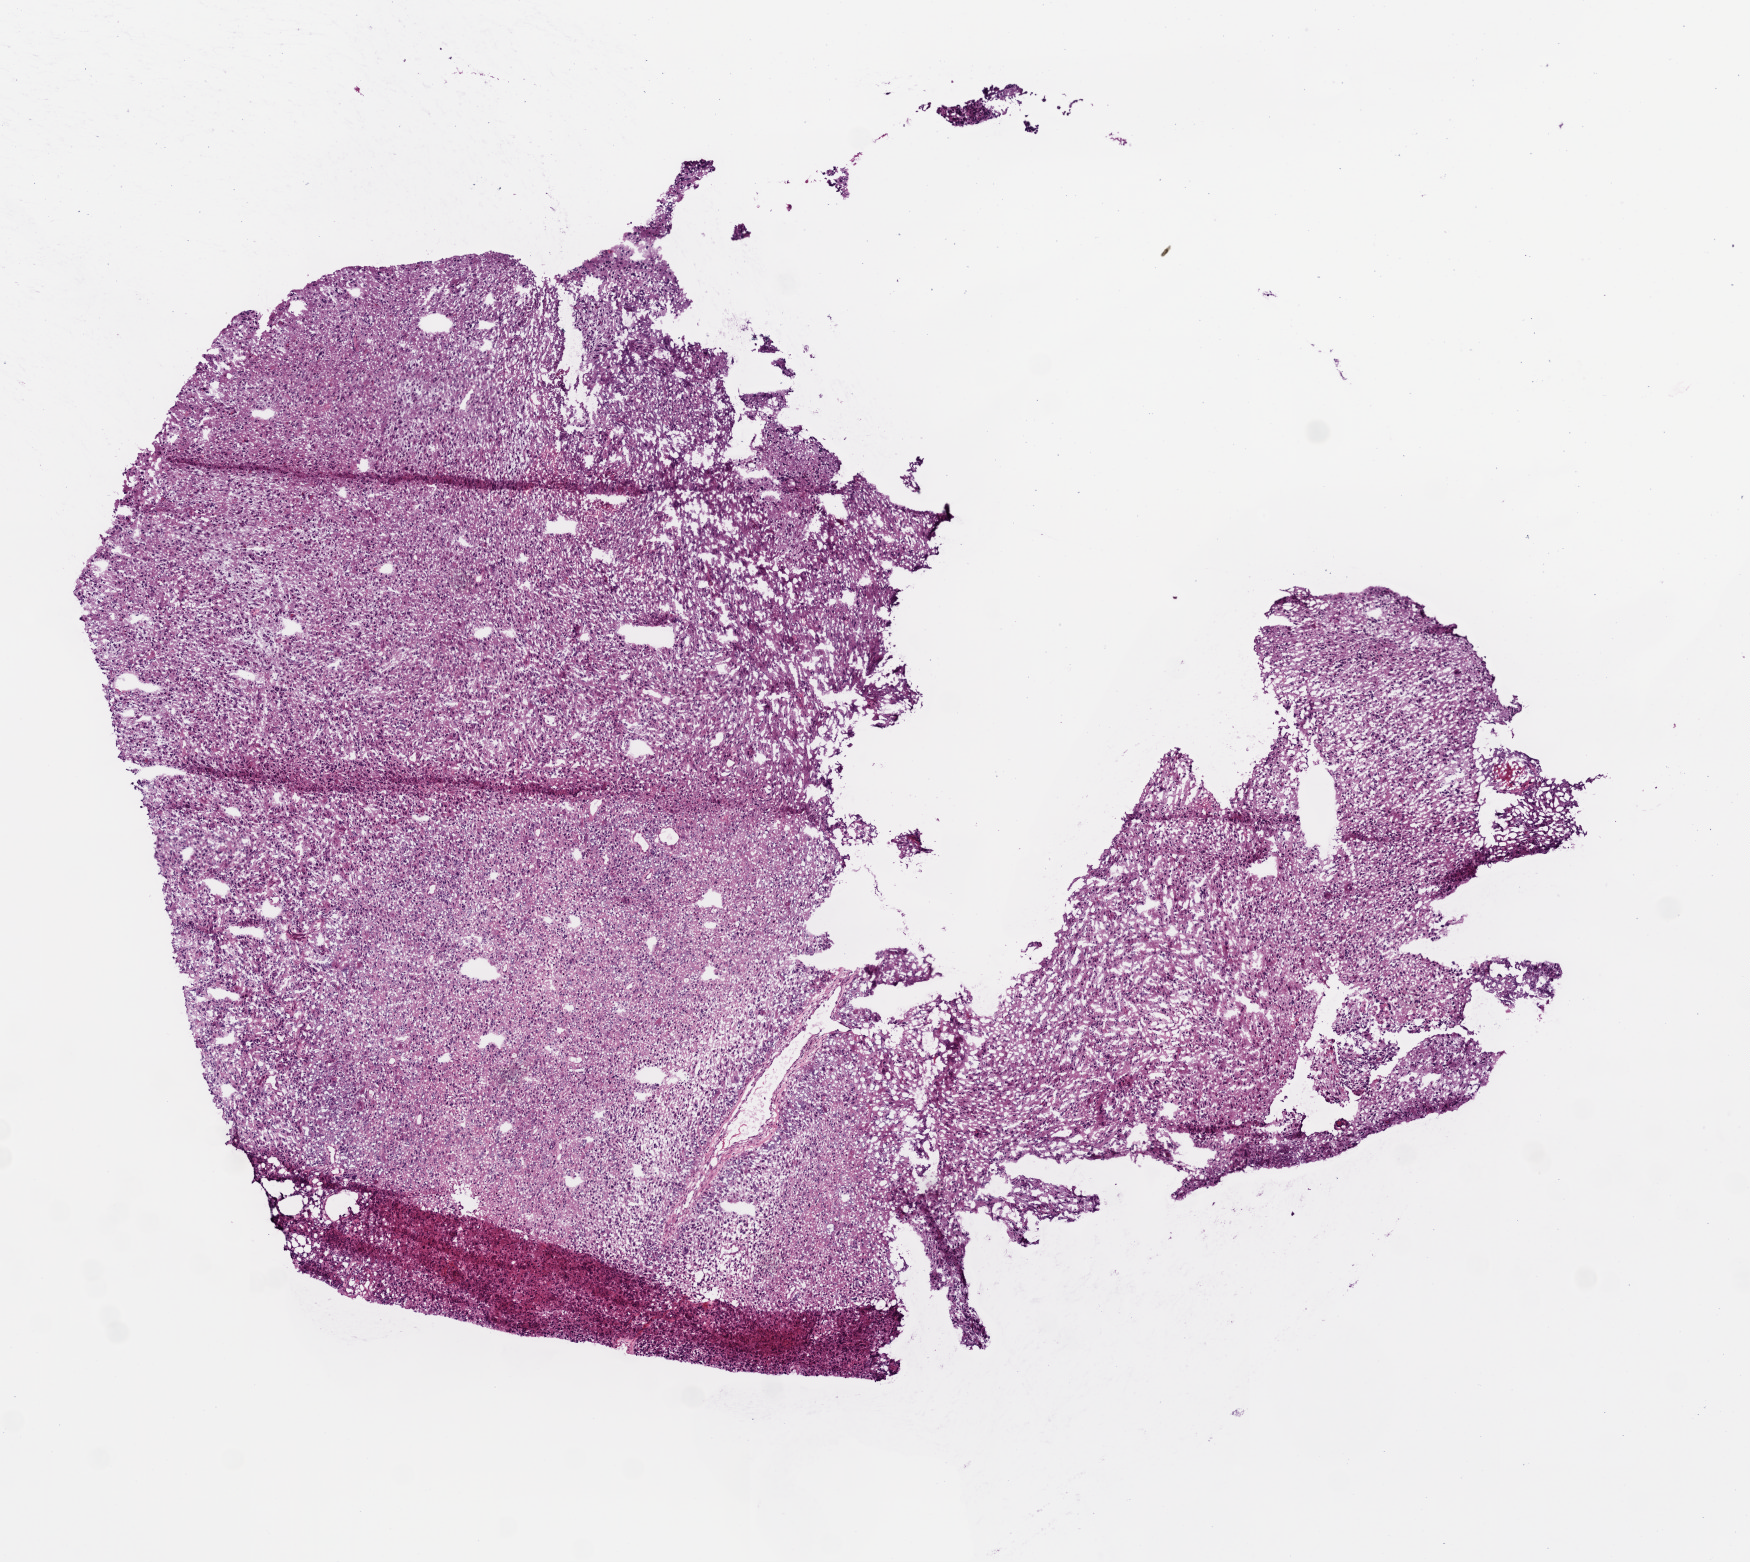
Digitized Hematoxylin and eosin (H&E) stained tissue section (whole slide) — low-resolution overview of the scanned area, about 7.0 x 6.3 mm (slide scanned at 20x); frozen section from the bottom of the tissue portion; sample: primary tumour, brain. Male, age 73 years at initial diagnosis. Composition of this section per pathologist review: tumour cells 100%, tumour nuclei 85%, normal cells 0%, stromal cells 0%, necrosis 0%.
- pathologic diagnosis: Glioblastoma